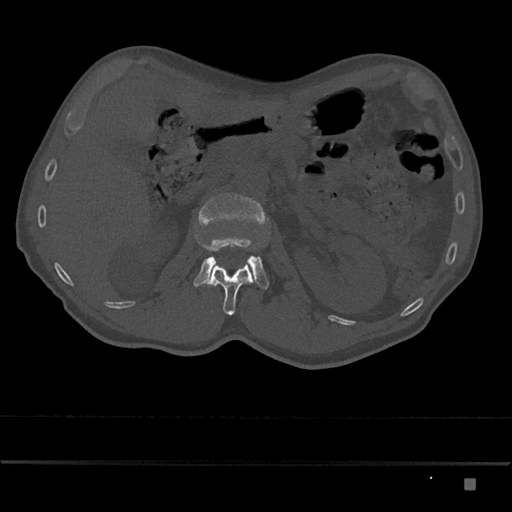
CT including the spine, one axial slice. 120 kVp. Bone window (W 1800 / L 400 HU). 0.5 mm slice thickness. 512 × 512 image matrix, field of view 390 × 390 mm. Male patient, age 72 years. Case-level facts recorded for this patient, not image findings: primary cancer: prostate.
Annotated regions visible in this slice (semi-automatic segmentation, software-assisted and operator-edited):
- L1 vertebra: bounding box (x1, y1, x2, y2) in pixels: (208, 262, 255, 315)
- L2 vertebra: (194, 193, 269, 289)